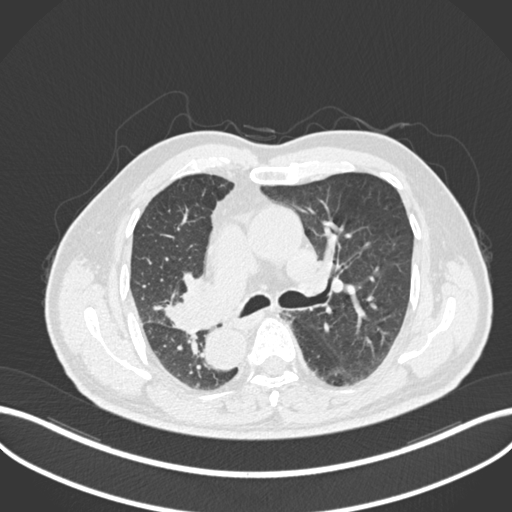
Chest CT, one axial slice; slice 140 of 206 in the series (ordered by position); 120 kVp; lung window (W 1500 / L -600 HU); 1 mm slice thickness; 512 × 512 image matrix, field of view 400 × 400 mm. Male patient, age 67 years. Case-level facts recorded for this patient, not image findings: clinical TNM (as recorded): T2a N0 M0.
Annotated regions visible in this slice (bounding box drawn by a radiologist):
- lung tumour (recorded histology: squamous cell carcinoma): bounding box (x1, y1, x2, y2) in pixels: (160, 271, 220, 334)